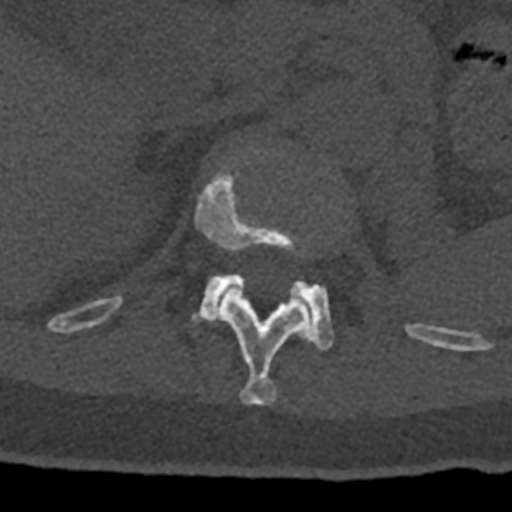
CT including the spine, one axial slice; slice 470 of 797 in the series (ordered by position); reconstruction kernel Br40s/3; bone window (W 1800 / L 400 HU); 512 × 512 image matrix, field of view 160 × 160 mm. Male patient, age 74 years. From the clinical record (not read from this slice): primary cancer: renal; vertebrae with lytic lesions (as recorded): T10, L1, L2, L3, L4, L5.
Structures marked on this image (semi-automatic segmentation, software-assisted and operator-edited):
- L1 vertebra: box from (x=192, y=274) to (x=334, y=351) px
- T12 vertebra: (x=70, y=158)–(x=432, y=405)